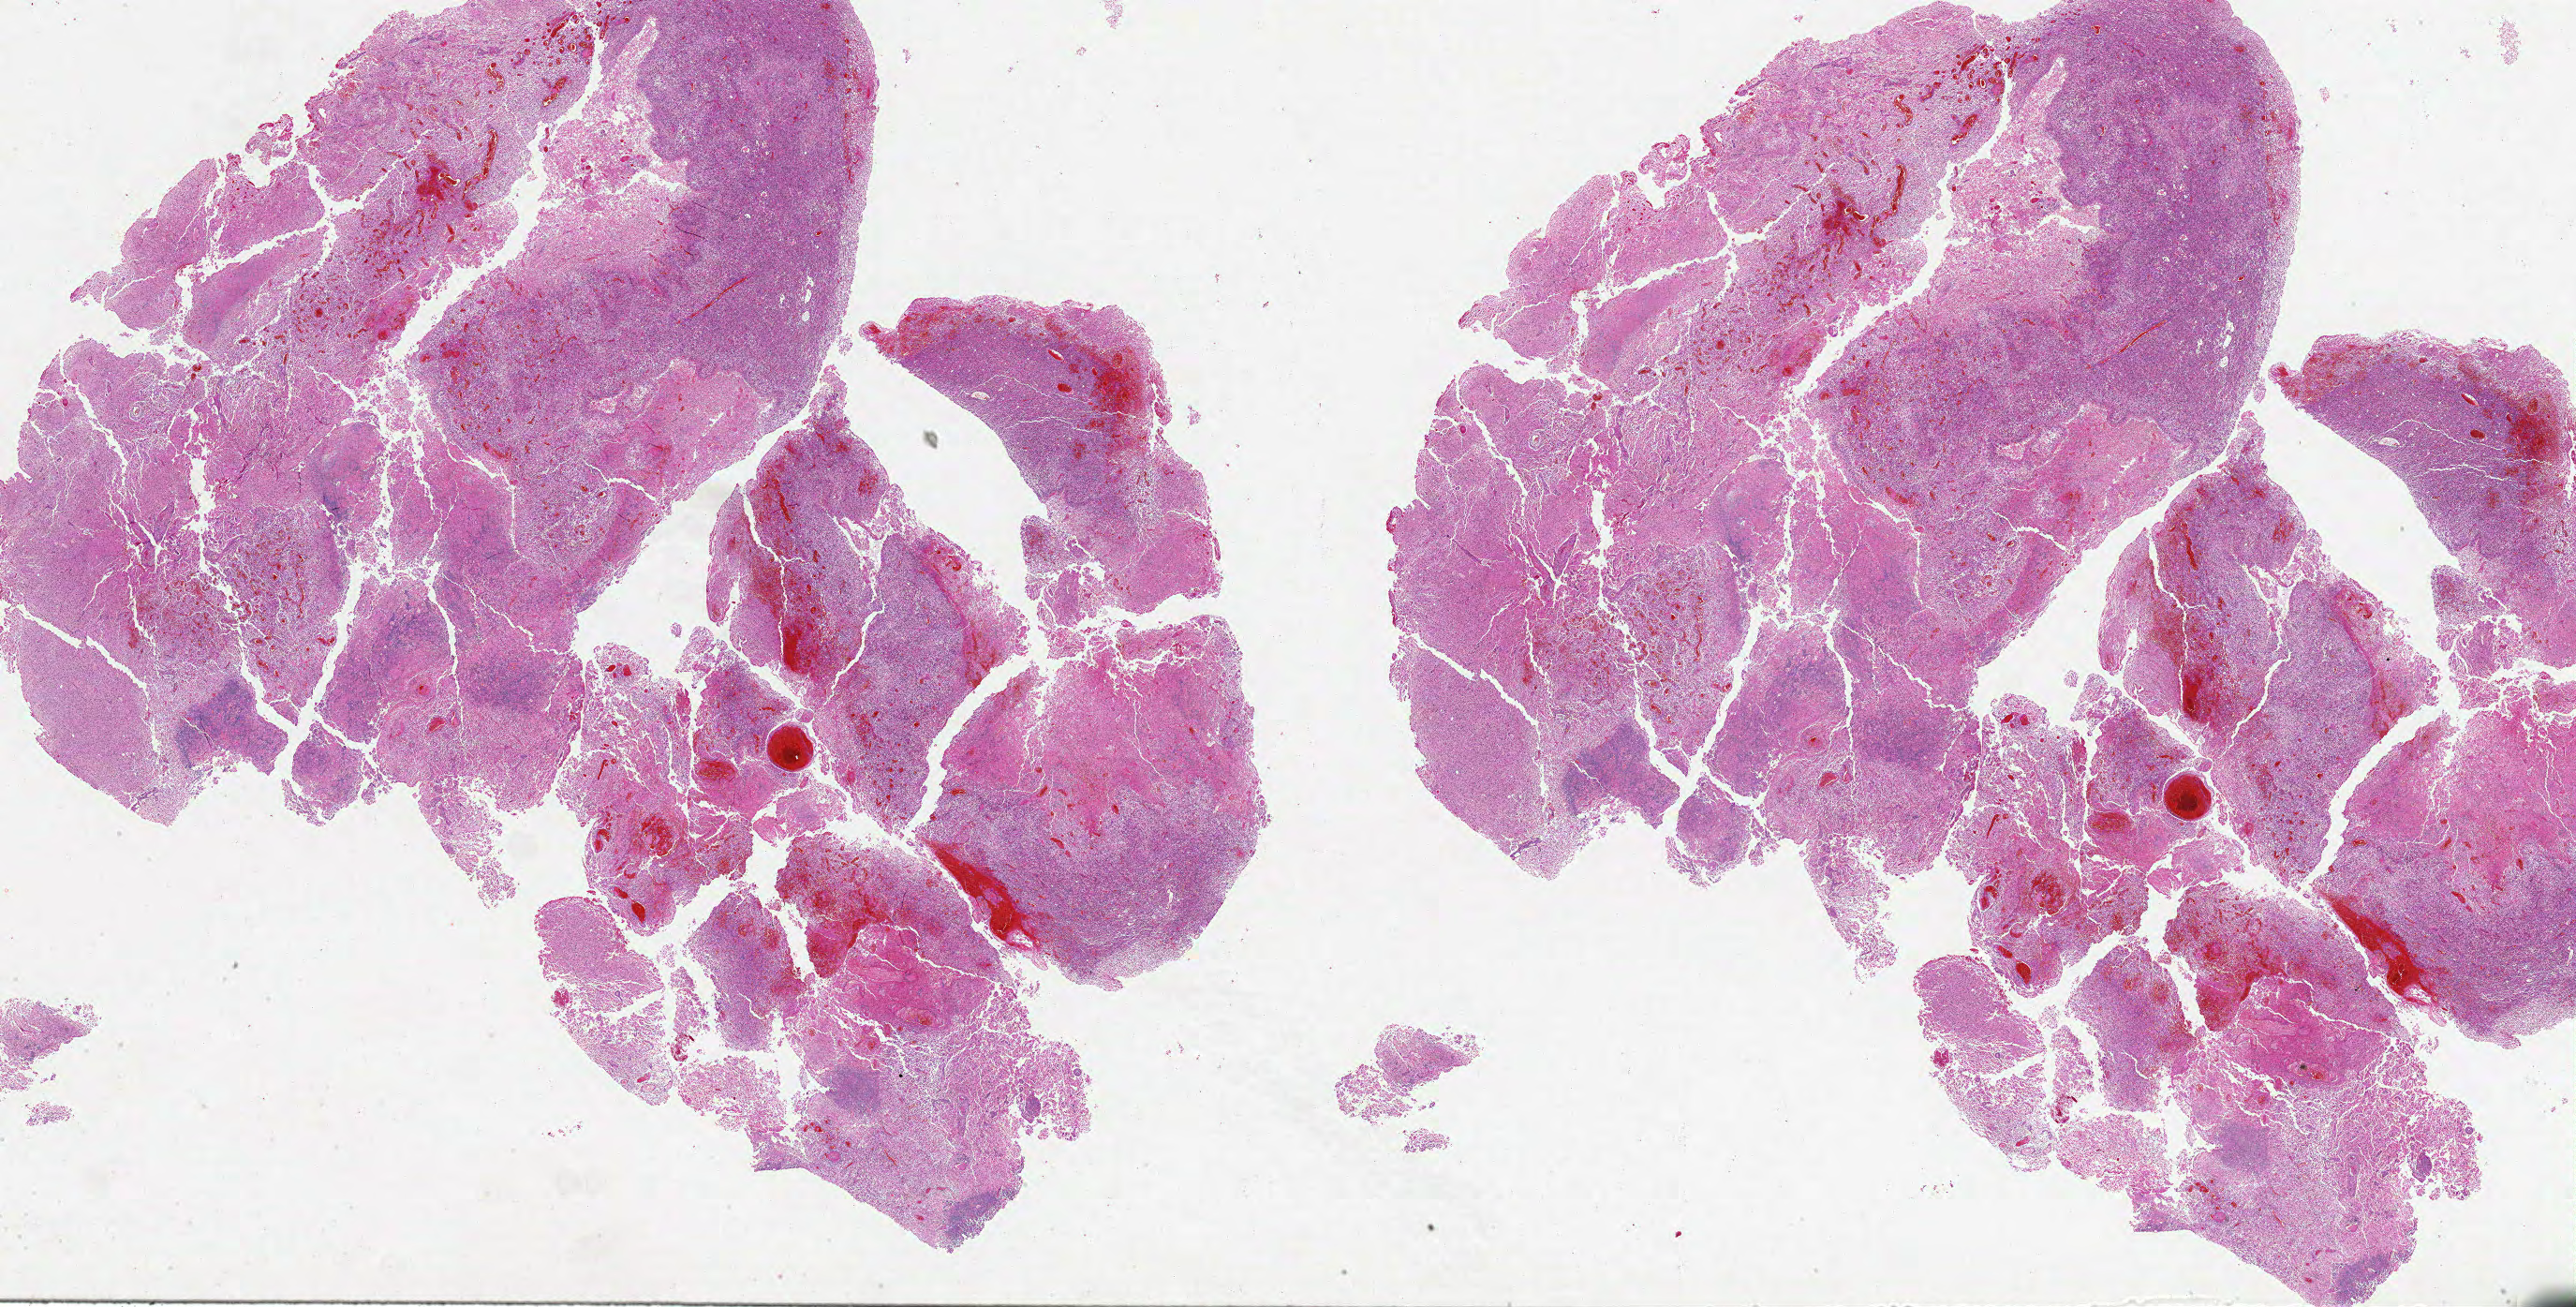
Whole-slide histology image, Hematoxylin and eosin (H&E) stained, low-resolution overview of the scanned area, about 44.0 x 22.3 mm (slide scanned at 20x), FFPE section, brain, primary tumour sample. Female, age 66 years at initial diagnosis.
• pathologic diagnosis: Glioblastoma